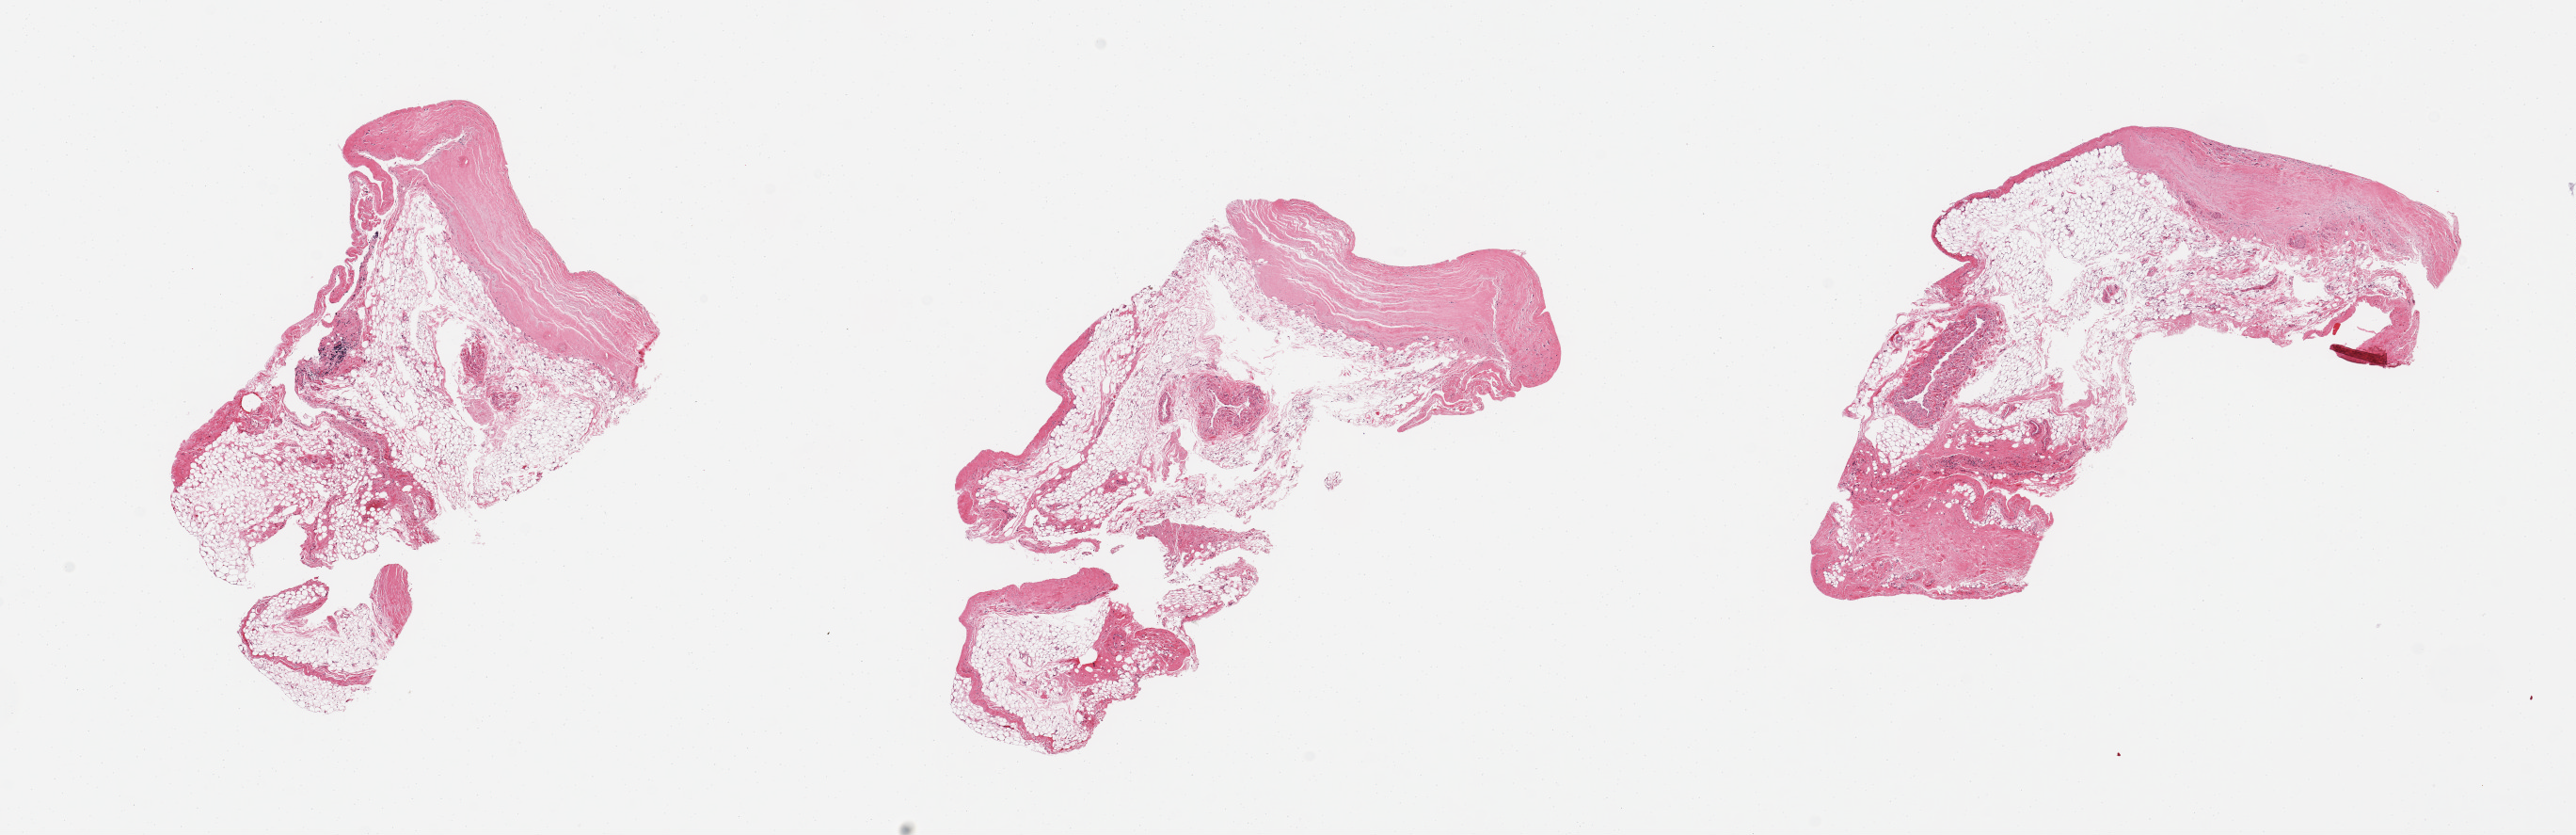
Whole-slide image, hematoxylin and eosin (H&E) stain — whole scanned area (about 21.7 x 7.0 mm) shown as a low-resolution overview; PAXgene-fixed paraffin-embedded (PFPE) section; section of aorta (target tissue); tissue donor sample. Donor sex: male.
Reviewer comment on this tissue sample: 3 pieces, no aorta; fat/connective tissue.